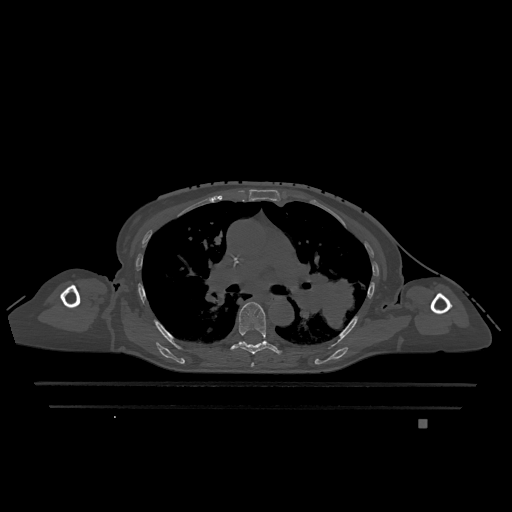
CT including the spine, one axial slice; position 789 of 1317 along the scan axis; bone window (W 1800 / L 400 HU); 512 × 512 image matrix, field of view 500 × 500 mm. Female patient, age 74 years. Case-level facts recorded for this patient, not image findings: primary cancer: lung.
Outlined on this slice (semi-automatically segmented with operator editing):
- T5 vertebra: bounding box [x1, y1, x2, y2] px = [251, 363, 254, 367]
- T6 vertebra: [231, 302, 281, 355]